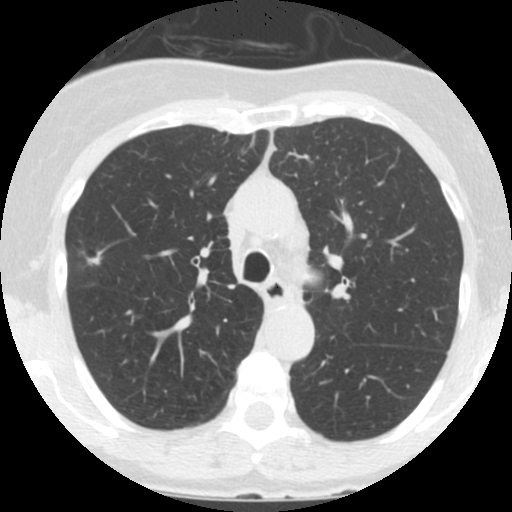
Axial slice from a low-dose chest CT screening exam. Third screening round (two years after baseline). Lung window (W 1500 / L -600 HU). 2.5 mm slice thickness. Slice 47 of 146 in the series. 512 × 512 image matrix. Female participant, aged 60 years at enrolment. Current smoker at enrolment.
Expert reader's lesion annotation, bounding box <65,232,113,284> (left, top, right, bottom; pixels). Reader record for this screening exam (exam-level; its link to the box is not recorded): non-calcified nodule or mass ≥4 mm, right upper lobe, 12 × 12 mm, smooth margins, ground glass attenuation, pre-existing on the prior screen: yes; interval growth: yes. Official screen result: positive, other. Participant outcome: lung cancer diagnosed 56 days after this screen — bronchiolo-alveolar adenocarcinoma, NOS, right upper lobe, well differentiated (G1), stage IA (AJCC 6th edition), 11 mm at pathology.